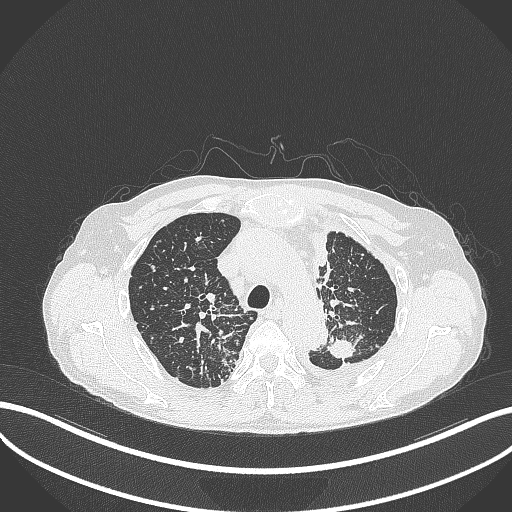
Chest CT, one axial slice. Position 265 of 325 along the scan axis. Reconstruction kernel B70f. 120 kVp. Lung window (W 1500 / L -600 HU). 1 mm slice thickness. 512 × 512 image matrix. Patient: male, 58 years. Case-level facts recorded for this patient, not image findings: clinical TNM (as recorded): T1c N3 M1.
Annotated regions visible in this slice (rectangle marked by the reading radiologist):
- lung tumour (recorded histology: adenocarcinoma): bounding box <323,335,356,361> (left, top, right, bottom; pixels)